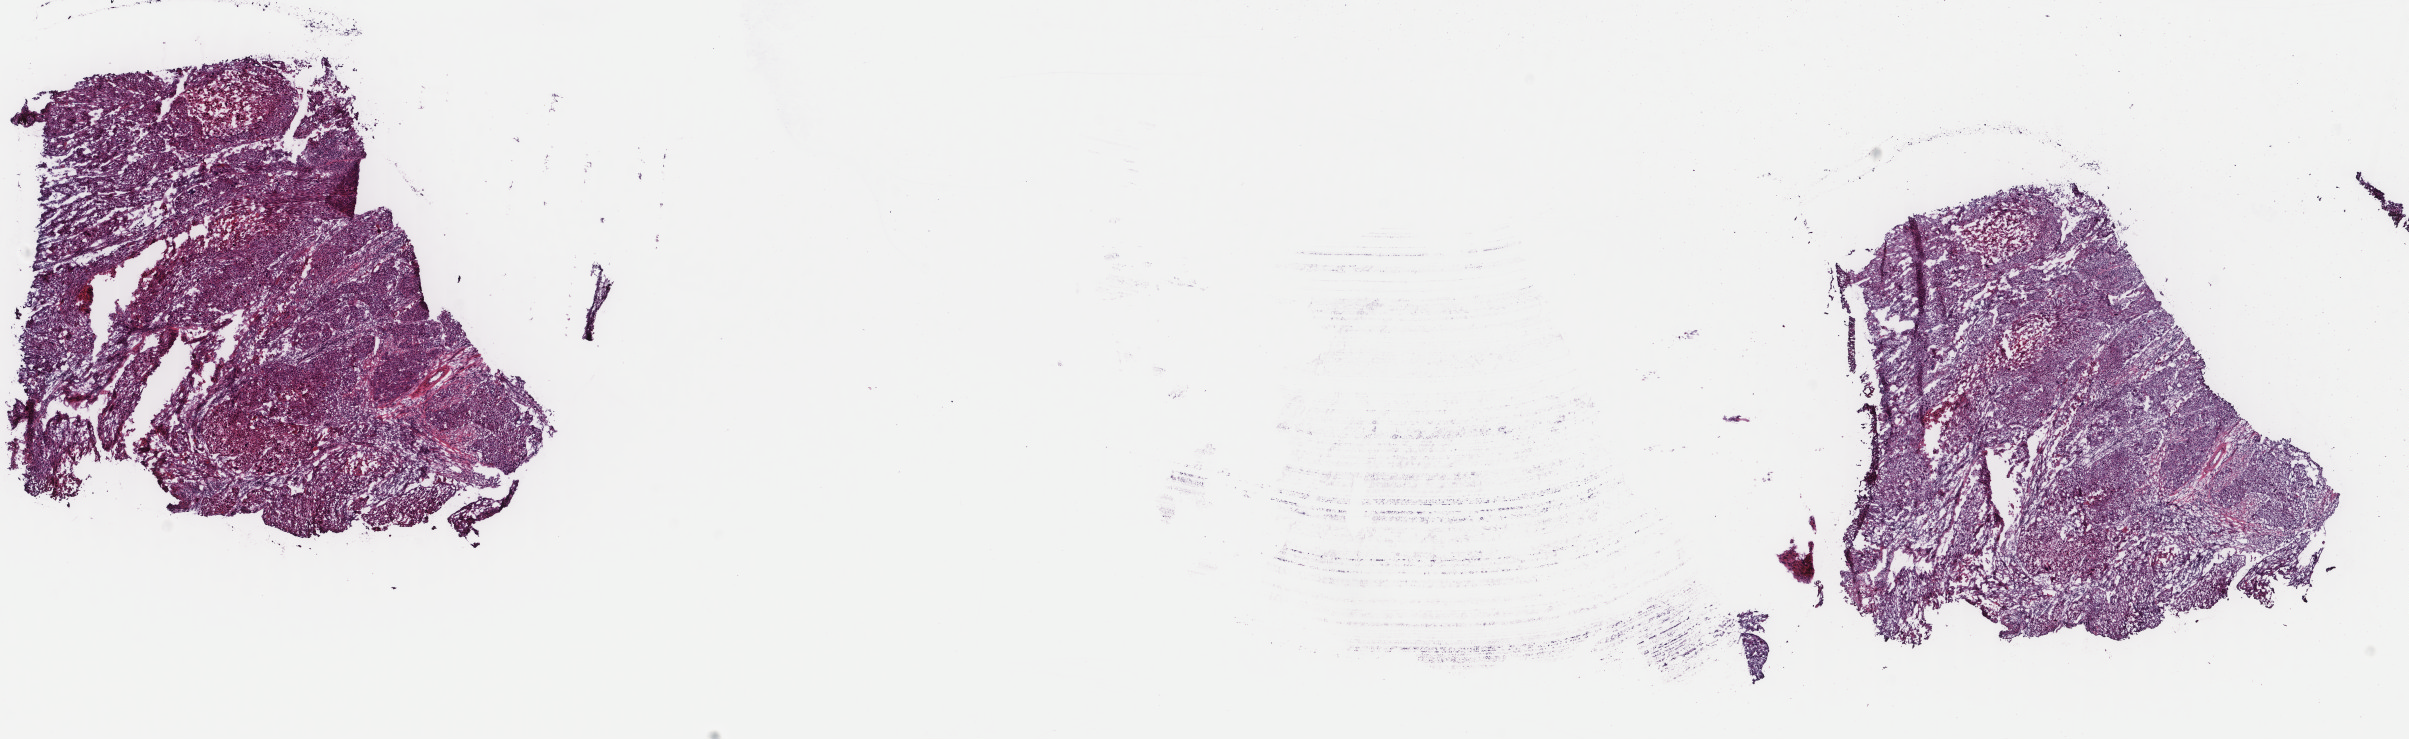
Whole-slide histology image, H&E-stained — whole scanned area (about 19.1 x 5.9 mm, slide scanned at 40x) shown as a low-resolution overview; frozen section from the top of the tissue portion; sample: primary tumour, cervix. Patient: female, age at initial diagnosis 45 years. Histologic grade: G2 (moderately differentiated). Composition of this section per pathologist review: tumour cells 80%, tumour nuclei 80%, normal cells 0%, stromal cells 10%, necrosis 10%. Infiltration values recorded for this section: lymphocyte infiltration 50%, monocyte infiltration 5%, neutrophil infiltration 30%.
FIGO stage: IB. Histologic diagnosis: Squamous cell carcinoma, NOS (cervix uteri).